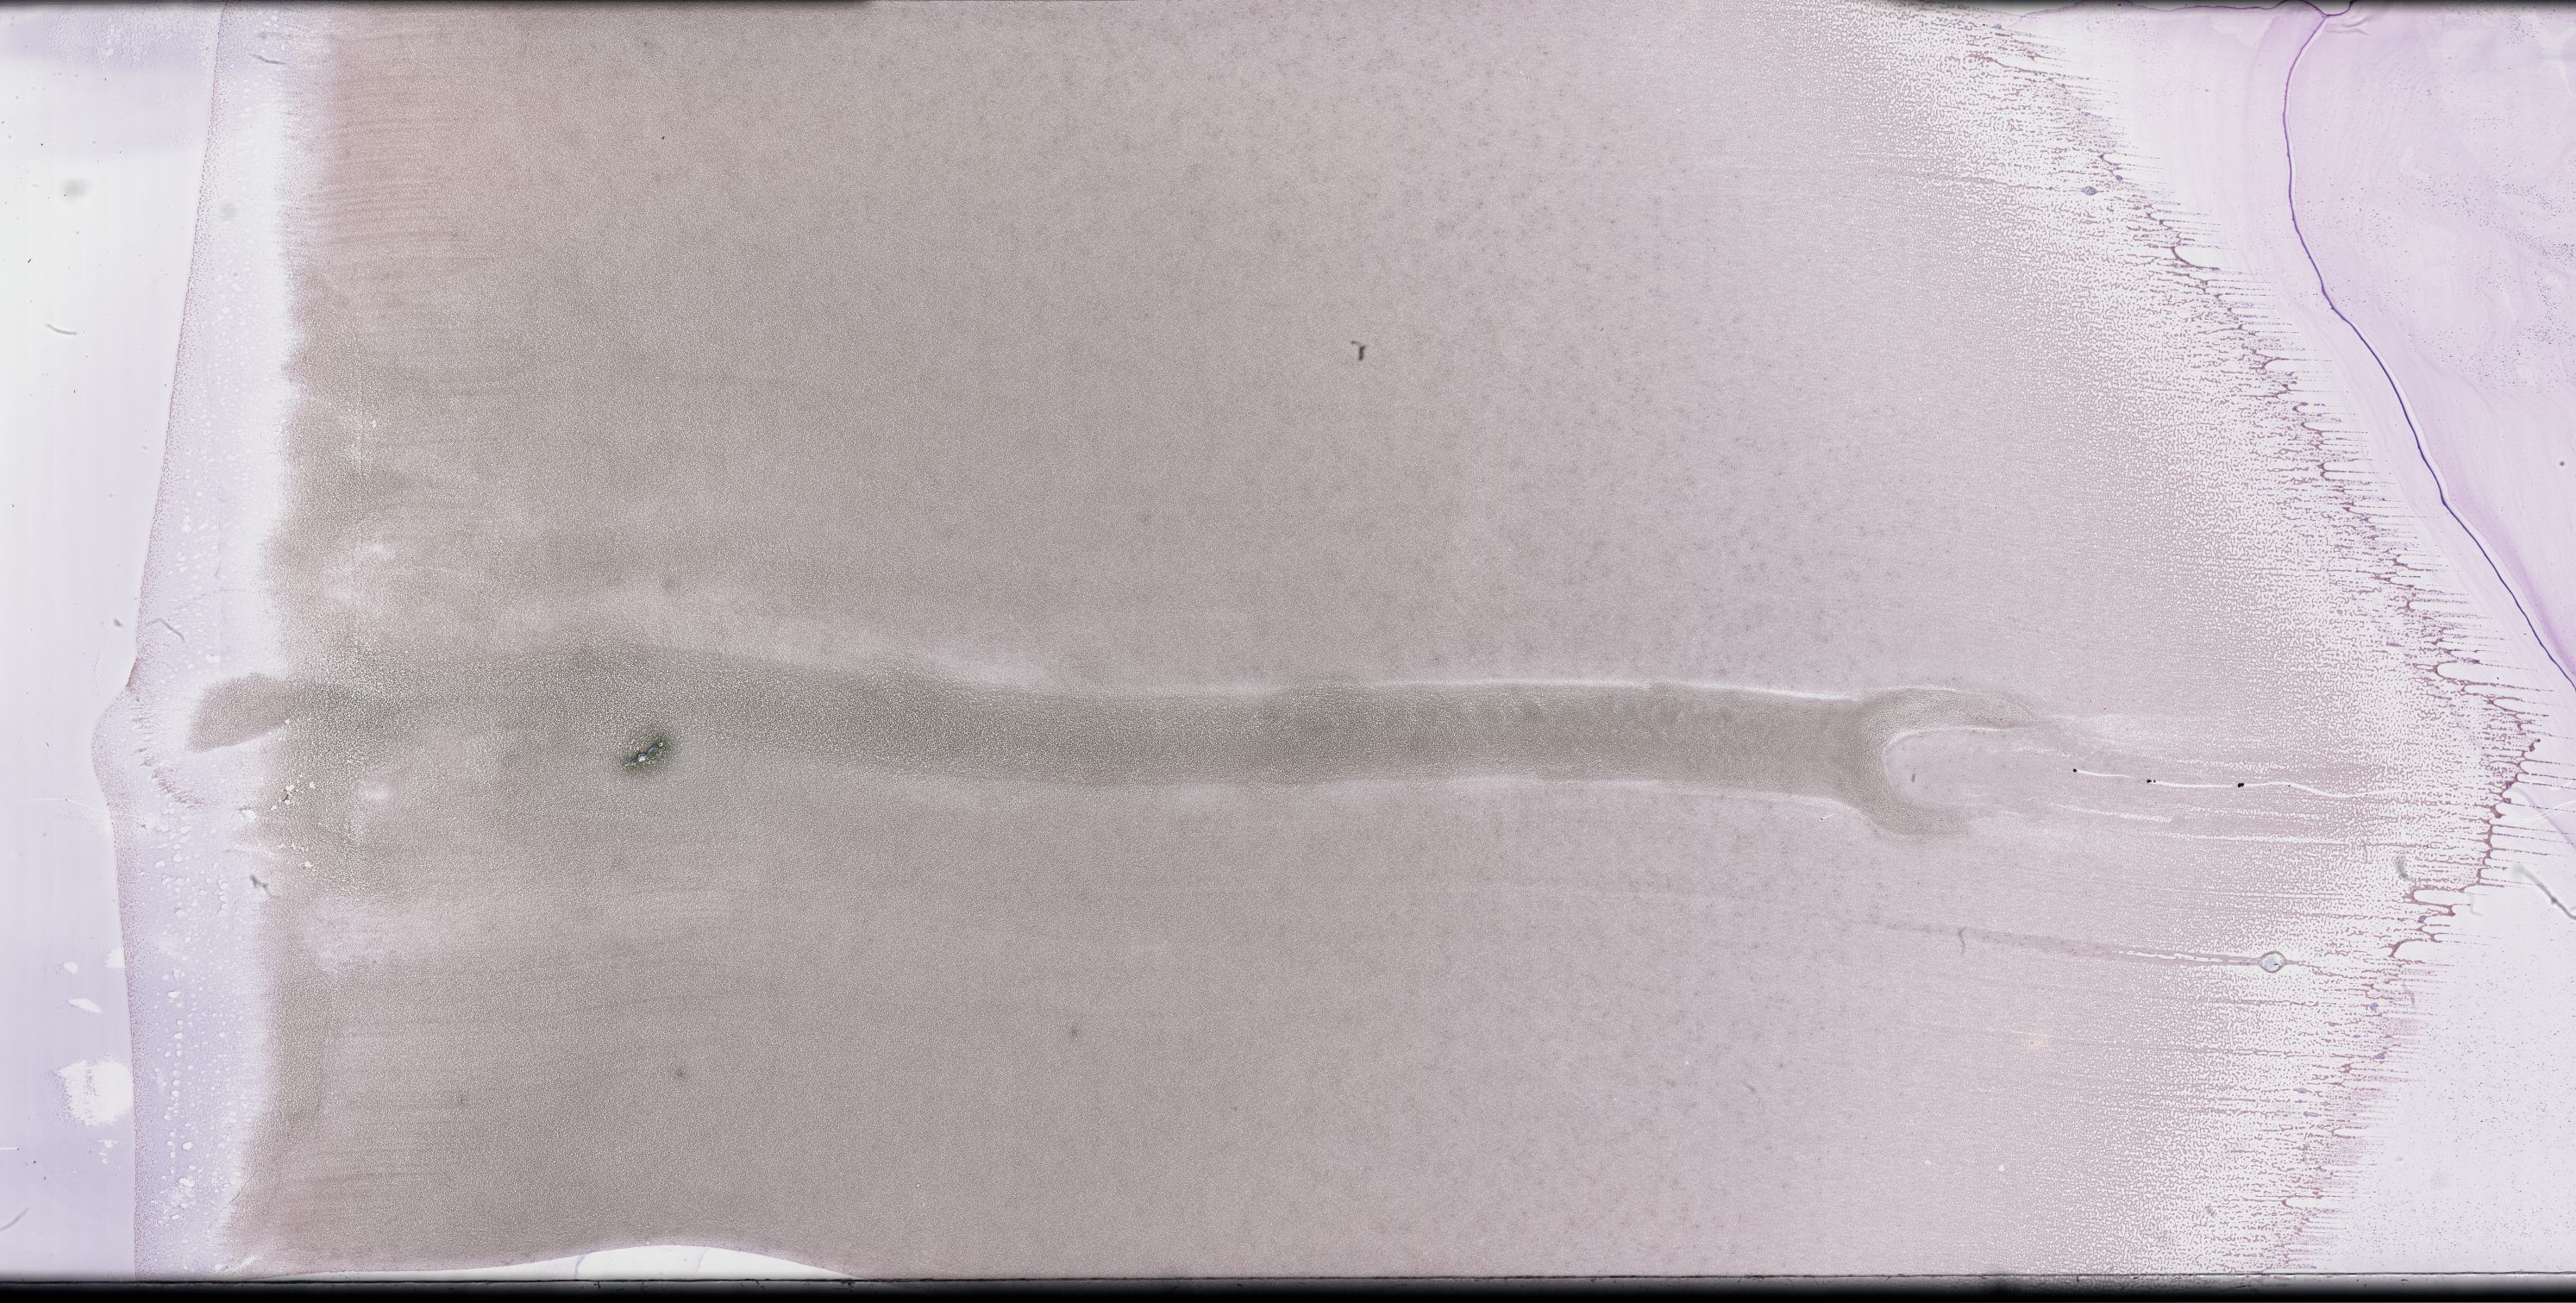
Wright-Giemsa-stained whole blood smear, whole-slide image — a low-resolution overview of the entire scanned area, about 48.2 x 24.4 mm. Smear from an EDTA sample. Patient: male.
From a patient with: Plasma Cell Myeloma.